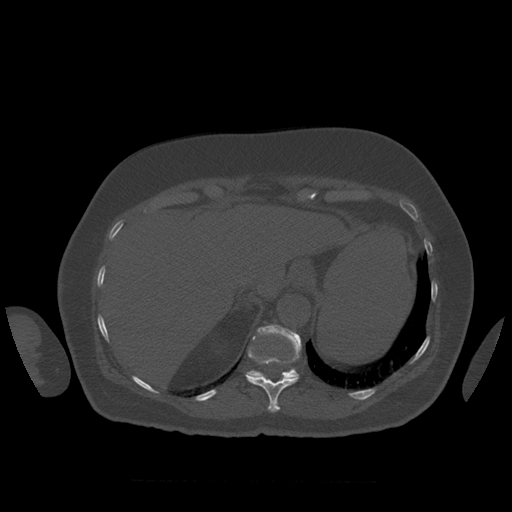
CT including the spine, one axial slice; position 315 of 399 along the scan axis; bone window (W 1800 / L 400 HU); 1.25 mm slice thickness; 512 × 512 image matrix, field of view 404 × 404 mm. Patient age 81 years. From the clinical record (not read from this slice): primary cancer: renal.
Structures marked on this image (semi-automatically segmented with operator editing):
- T11 vertebra: bounding box <246,337,298,412> (left, top, right, bottom; pixels)
- T12 vertebra: <246,325,302,380>